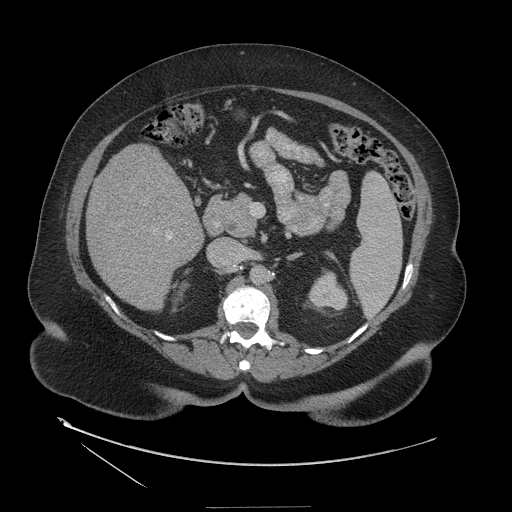
Contrast-enhanced abdominal CT (liver protocol), one axial slice; position 60 of 127 along the scan axis; reconstruction kernel STANDARD; soft-tissue window (W 400 / L 40 HU); 2.5 mm slice thickness; 512 × 512 image matrix, field of view 480 × 480 mm. Case-level facts recorded for this patient, not image findings: diagnosis: hepatocellular carcinoma (patient treated with transarterial chemoembolisation; whether this scan precedes or follows treatment is not stated here); TNM stage (as recorded): Stage-II; Child-Pugh class: A; tumour differentiation: well differentiated; tumour size: 3 cm.
Outlined on this slice (semi-automatic segmentation, software-assisted and operator-edited):
- liver parenchyma outside the tumour (the mass and vessels are separate outlines, so this box may not span the whole liver): box from (x=86, y=144) to (x=204, y=310) px
- liver vessels: (x=167, y=235)–(x=171, y=239)